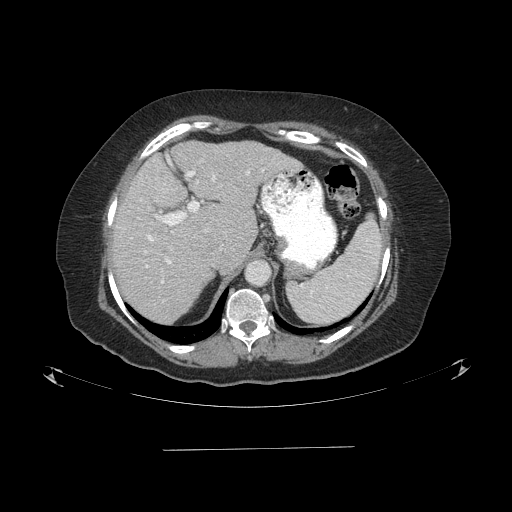
Contrast-enhanced abdominal CT (liver protocol), one axial slice. Slice 61 of 103 in the series (ordered by position). Reconstruction kernel STANDARD. 120 kVp. One of 2 acquisitions stored at this slice position. Soft-tissue window (W 400 / L 40 HU). 2.5 mm slice thickness. 512 × 512 image matrix, field of view 500 × 500 mm. Case-level facts recorded for this patient, not image findings: diagnosis: hepatocellular carcinoma (patient treated with transarterial chemoembolisation; whether this scan precedes or follows treatment is not stated here); TNM stage (as recorded): Stage-IIIA; Child-Pugh class: A; tumour differentiation: poorly differentiated.
Annotated regions visible in this slice (semi-automatic segmentation, software-assisted and operator-edited):
- abdominal aorta: box from (x=247, y=262) to (x=269, y=284) px
- liver parenchyma outside the tumour (the mass and vessels are separate outlines, so this box may not span the whole liver): (x=110, y=140)–(x=300, y=322)
- liver vessels: (x=144, y=160)–(x=264, y=283)